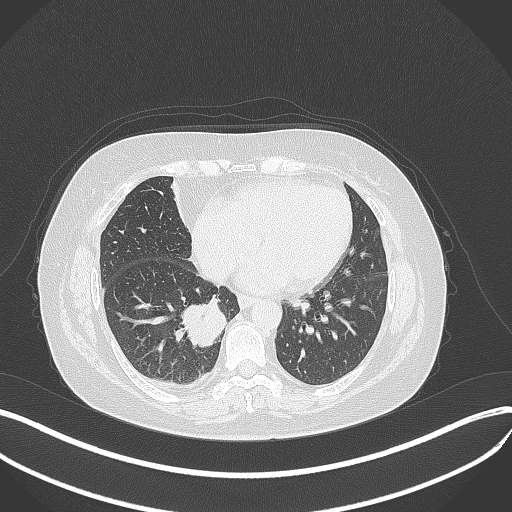
Chest CT, one axial slice; slice 133 of 381 in the series (ordered by position); reconstruction kernel B70f; 120 kVp; lung window (W 1500 / L -600 HU); 1 mm slice thickness; 512 × 512 image matrix. Patient: female, 56 years. From the clinical record (not read from this slice): clinical TNM (as recorded): T2b N1 M0; histopathological grade: G3.
Outlined on this slice (bounding box drawn by a radiologist):
- lung tumour (recorded histology: small cell carcinoma): bounding box <173,299,230,347> (left, top, right, bottom; pixels)